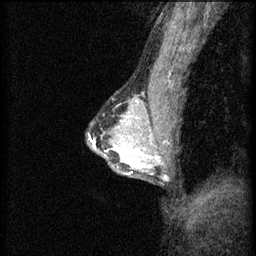
Breast MRI (dynamic contrast-enhanced), one sagittal slice. Position 40 of 60 along the scan axis. 3 images stored at this slice position (order not interpretable as contrast timing). 1.5 T. TE 4.2 ms, TR 8.2 ms. 2 mm slice thickness. 256 × 256 image matrix. Patient: female, 44 years.
Annotated regions visible in this slice (semi-automatically segmented with operator editing):
- analysis volume of interest (the breast-tissue region the enhancement analysis was run in; not a lesion): bounding box [x1, y1, x2, y2] px = [102, 132, 151, 173]
- tumour enhancement mask (voxels above the 70 % enhancement threshold inside the analysis volume of interest): [106, 136, 151, 173]